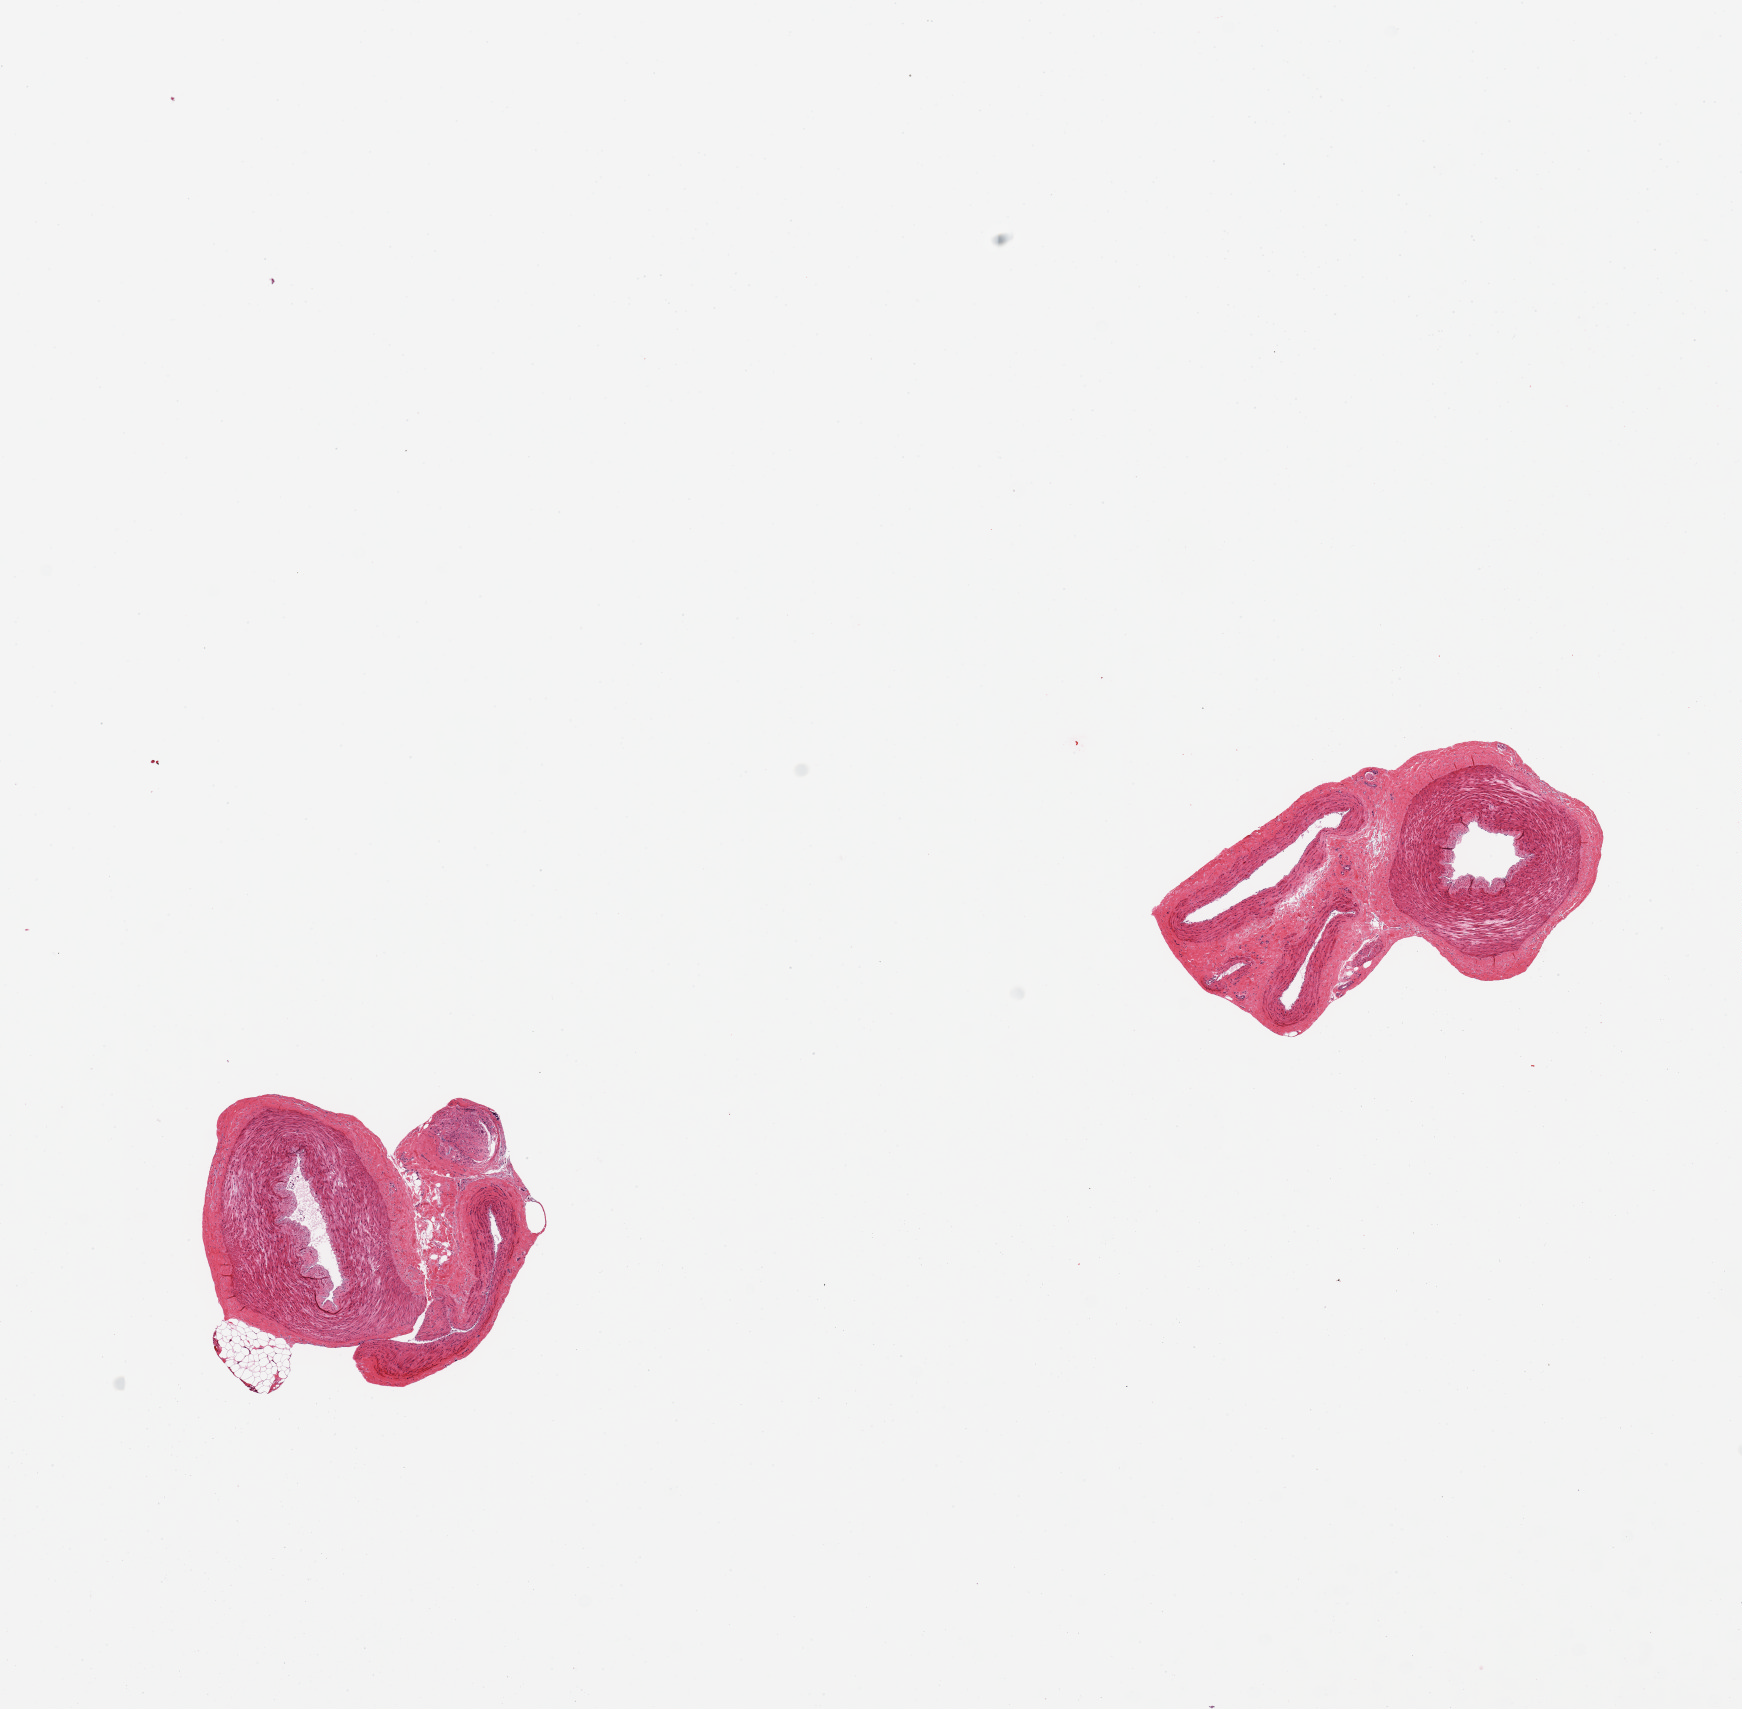
Haematoxylin and eosin whole-slide image, brightfield, whole scanned area (about 13.8 x 13.5 mm, from a 20x scan) shown as a low-resolution overview, PAXgene-fixed paraffin-embedded (PFPE) section, sampled site (target tissue): tibial artery, tissue donor sample.
• reviewer comment on this tissue sample: 2 pieces, clean specimens, no adherent fat